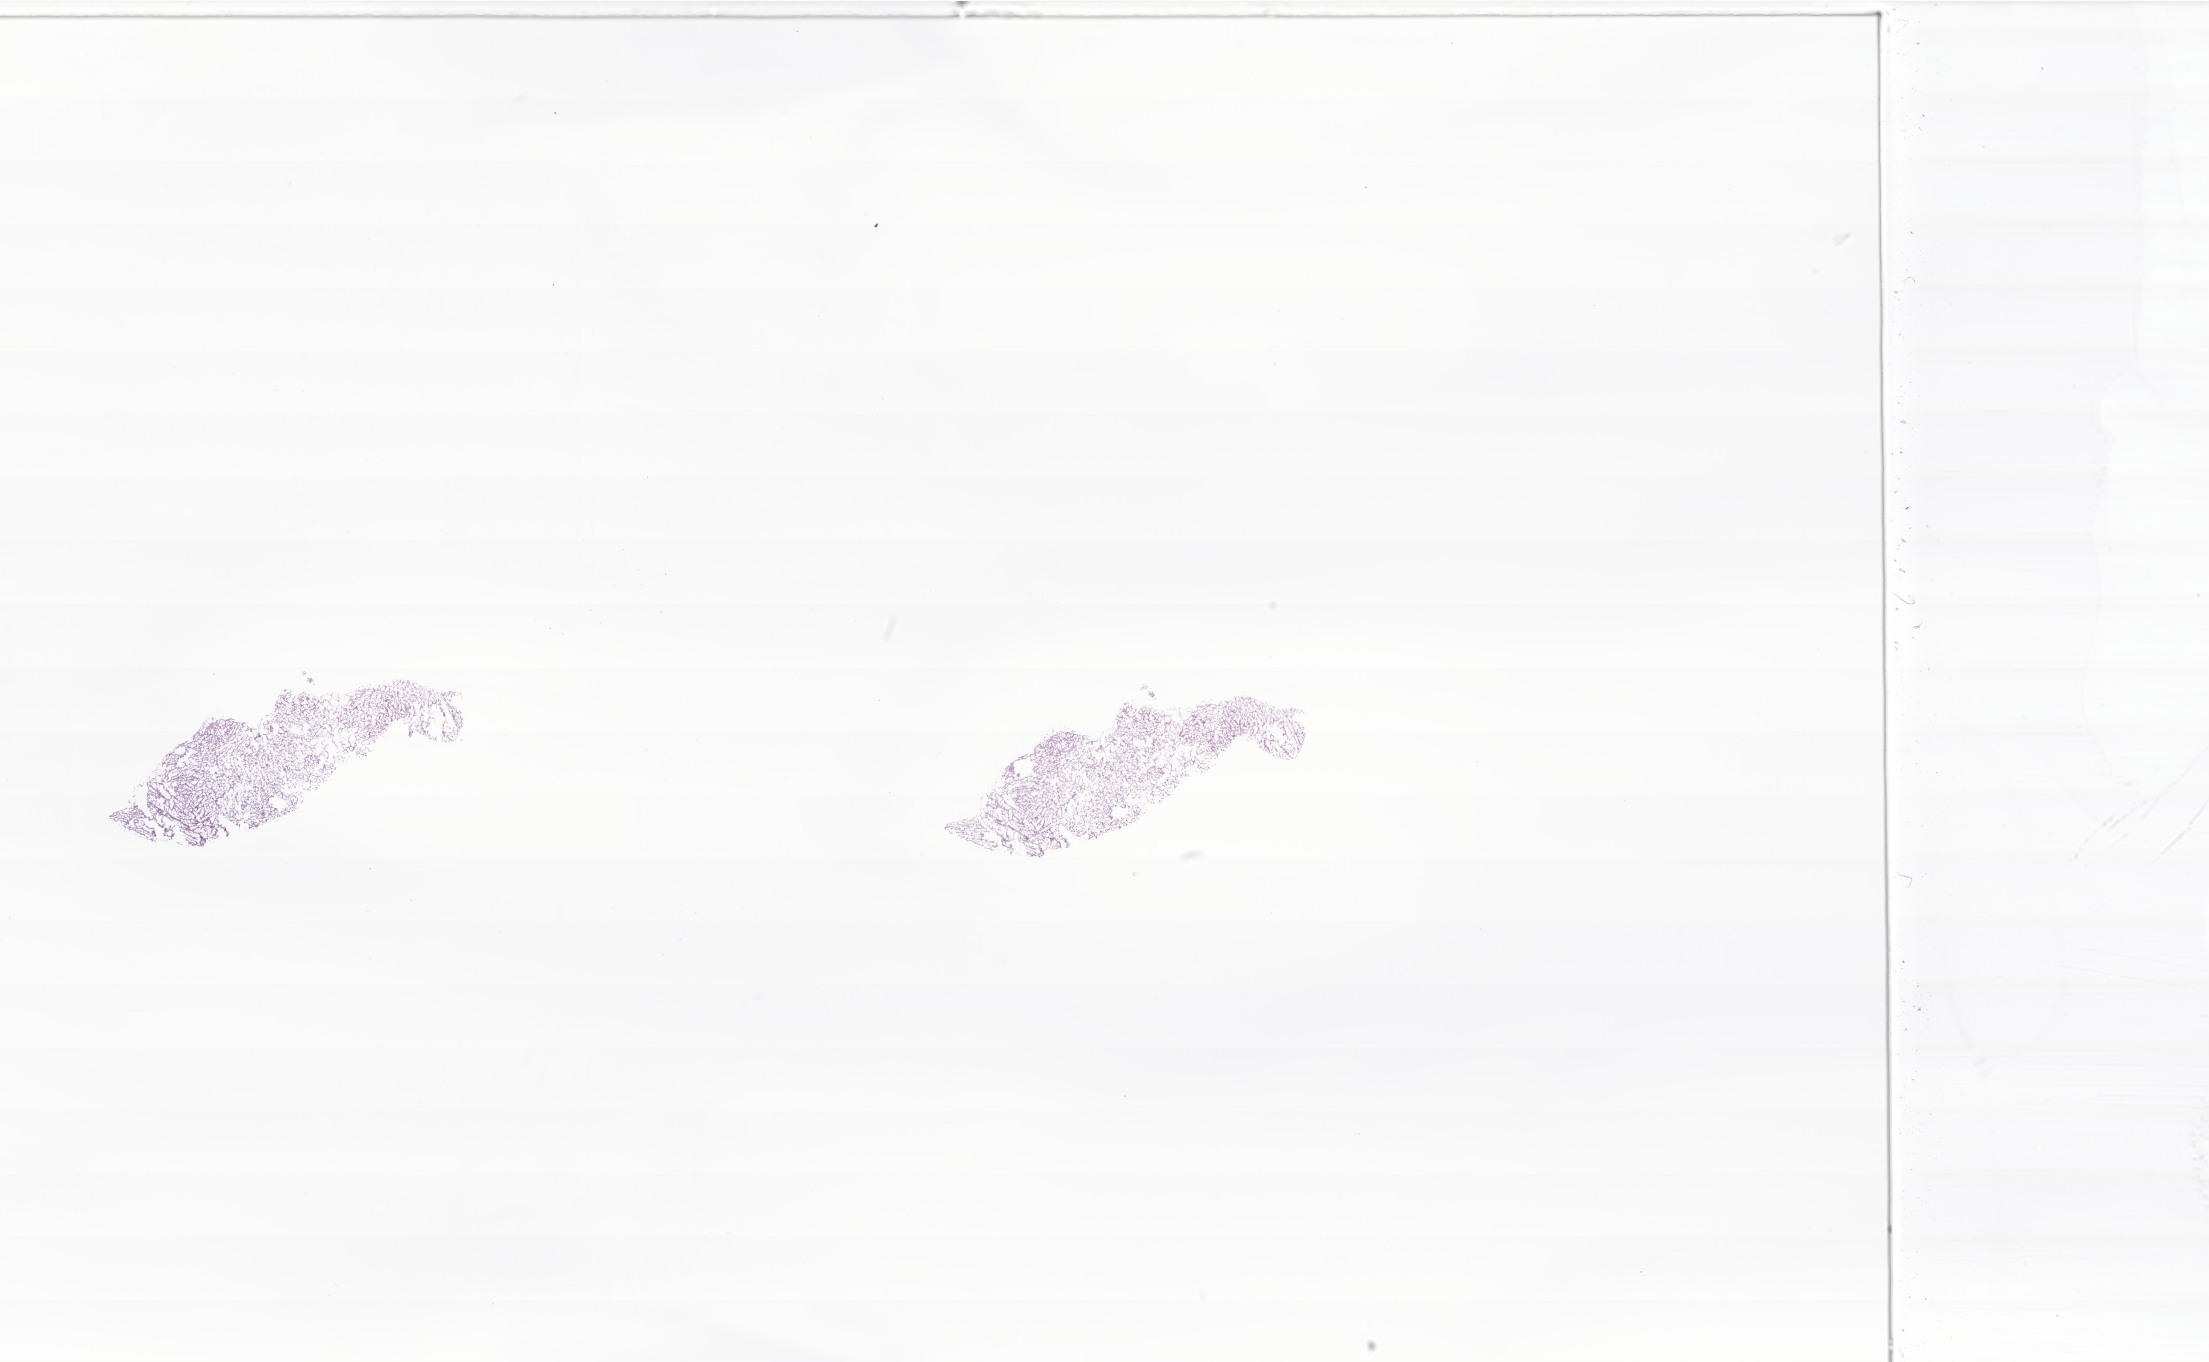
H&E whole-slide image of tumor tissue from the brain — a low-resolution overview of the entire scanned area, about 37.3 x 23.0 mm, frozen section (OCT-embedded). Male patient, age 52 months.
Recorded diagnosis: Ependymoma, NOS.